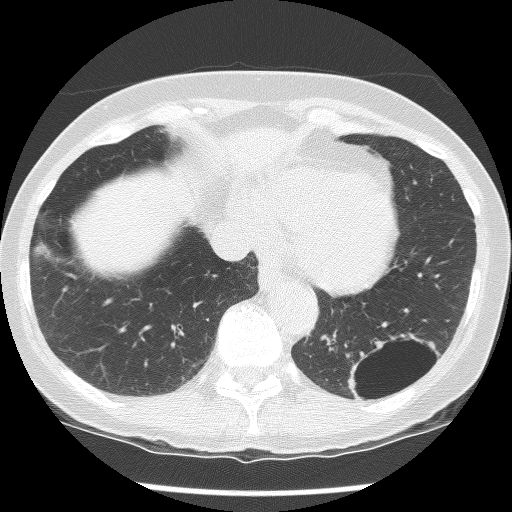
Axial slice from a low-dose chest CT screening exam; second screening round (one year after baseline); lung window (W 1500 / L -600 HU); slice 97 of 136 in the series. Female participant, aged 61 years at enrolment. Current smoker at enrolment.
• Lesion marked by an expert reader, box from (x=330, y=319) to (x=439, y=415) px.
• The screening reader recorded 2 non-calcified nodules or masses ≥4 mm on this exam; which of them this box marks is not recorded.
• Participant outcome: lung cancer diagnosed 585 days after this screen — non-small cell carcinoma, left lower lobe, poorly differentiated (G3), stage IB (AJCC 6th edition), 100 mm at pathology.